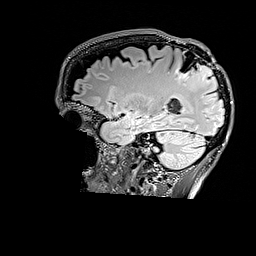
Brain MRI from a brain-tumour surgery series, one sagittal slice; slice 117 of 176 in the series (ordered by position); T2 FLAIR; 256 × 256 image matrix. From the clinical record (not read from this slice): histopathology: Astrocytoma; WHO grade: 3; IDH mutation: yes; tumour location: Right Parietal.
Outlined on this slice (outlined manually by an expert reader):
- tumour: box from (x=176, y=64) to (x=212, y=80) px
- tumour: (x=198, y=67)–(x=212, y=80)